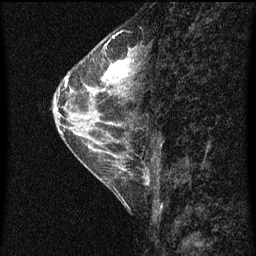
Breast MRI (dynamic contrast-enhanced), one sagittal slice; slice 27 of 60 in the series (ordered by position); dynamic contrast-enhanced series, image 2 of 4 at this slice position (ordered by acquisition); 1.5 T; TE 4.2 ms, TR 8 ms; 2 mm slice thickness; 256 × 256 image matrix, field of view 180 × 180 mm. Patient: female, 56 years.
Annotated regions visible in this slice (semi-automatic segmentation, software-assisted and operator-edited):
- analysis volume of interest (the breast-tissue region the enhancement analysis was run in; not a lesion): box from (x=56, y=52) to (x=135, y=115) px
- tumour enhancement mask (voxels above the 70 % enhancement threshold inside the analysis volume of interest): (x=66, y=62)–(x=129, y=85)